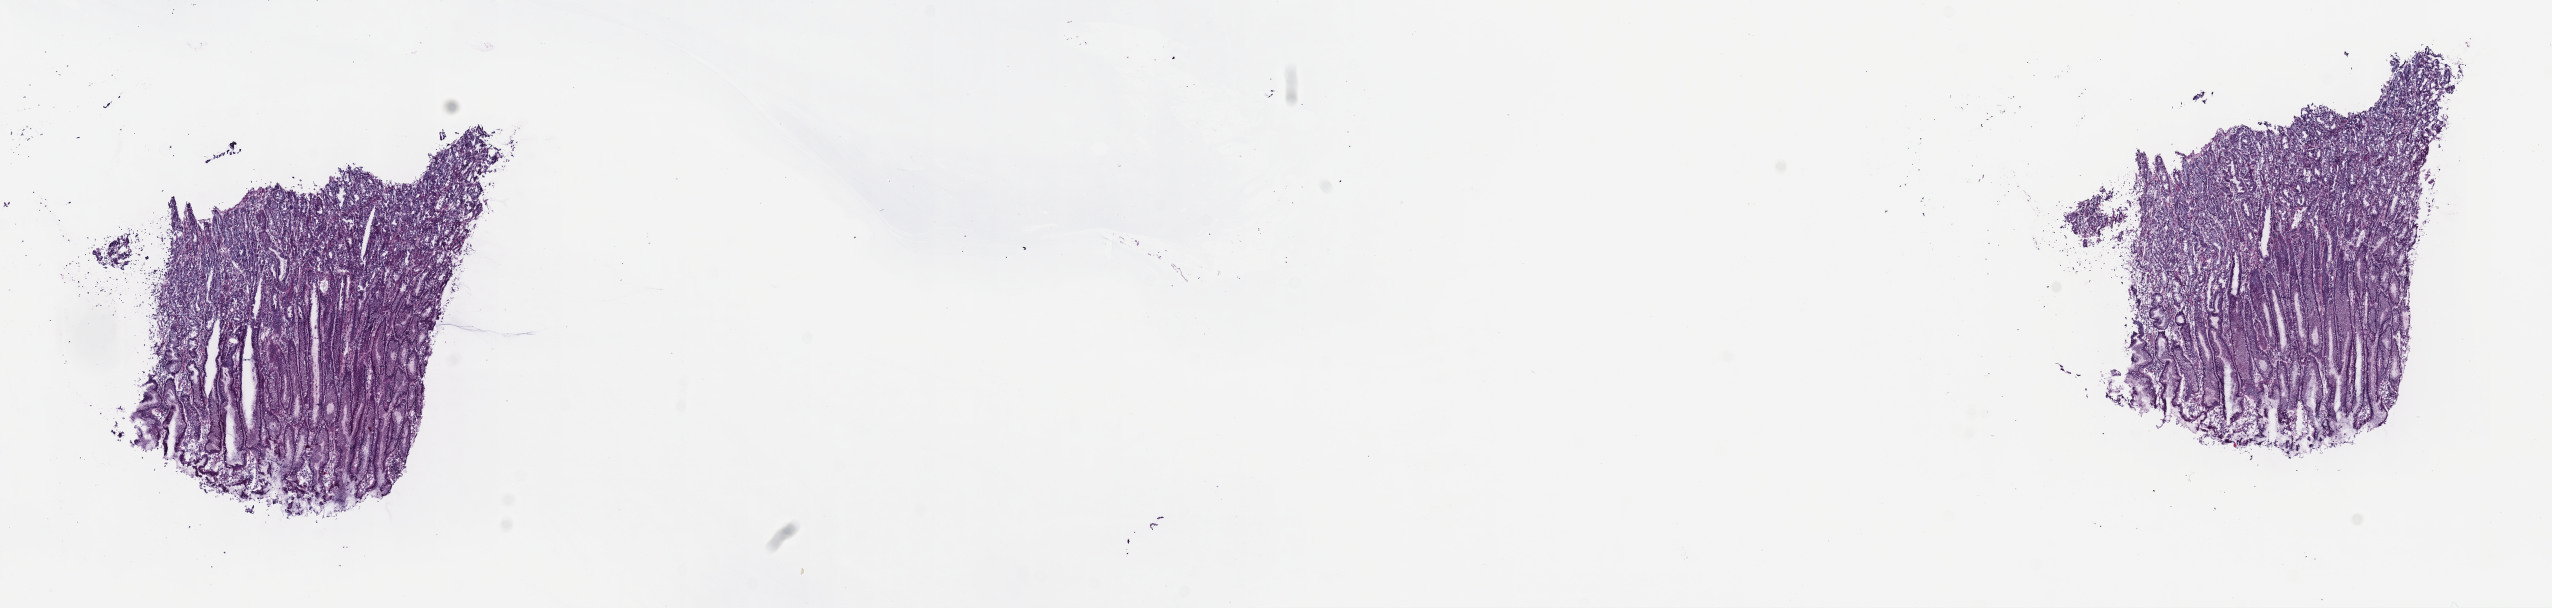
Digitized H&E-stained tissue section (whole slide) — a low-resolution overview of the entire scanned area, about 20.6 x 4.9 mm (from a 40x scan); frozen section from the top of the tissue portion; sample: primary tumour, esophagus. Patient: male, age at initial diagnosis 77 years. Histologic grade: G3 (poorly differentiated). Composition of this section per pathologist review: tumour cells 60%, tumour nuclei 60%, normal cells 20%, stromal cells 20%, necrosis 0%. Infiltration values recorded for this section: lymphocyte infiltration 40%, monocyte infiltration 20%, neutrophil infiltration 20%.
TNM: T1 N1 M0. Pathologic diagnosis: Adenocarcinoma, NOS (lower third of esophagus). AJCC pathologic stage: IIB.